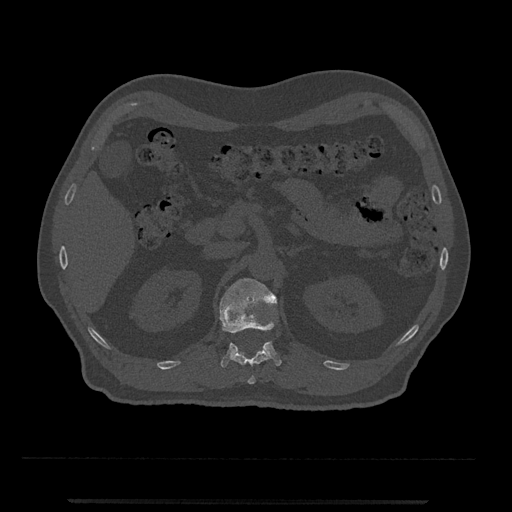
CT including the spine, one axial slice; position 367 of 797 along the scan axis; reconstruction kernel Br40s/3; bone window (W 1800 / L 400 HU); 512 × 512 image matrix, field of view 419 × 419 mm. Male patient, age 63 years. Case-level facts recorded for this patient, not image findings: primary cancer: prostate.
Structures marked on this image (semi-automatically segmented with operator editing):
- L1 vertebra: bounding box [x1, y1, x2, y2] px = [219, 278, 282, 368]
- T12 vertebra: [231, 348, 270, 384]